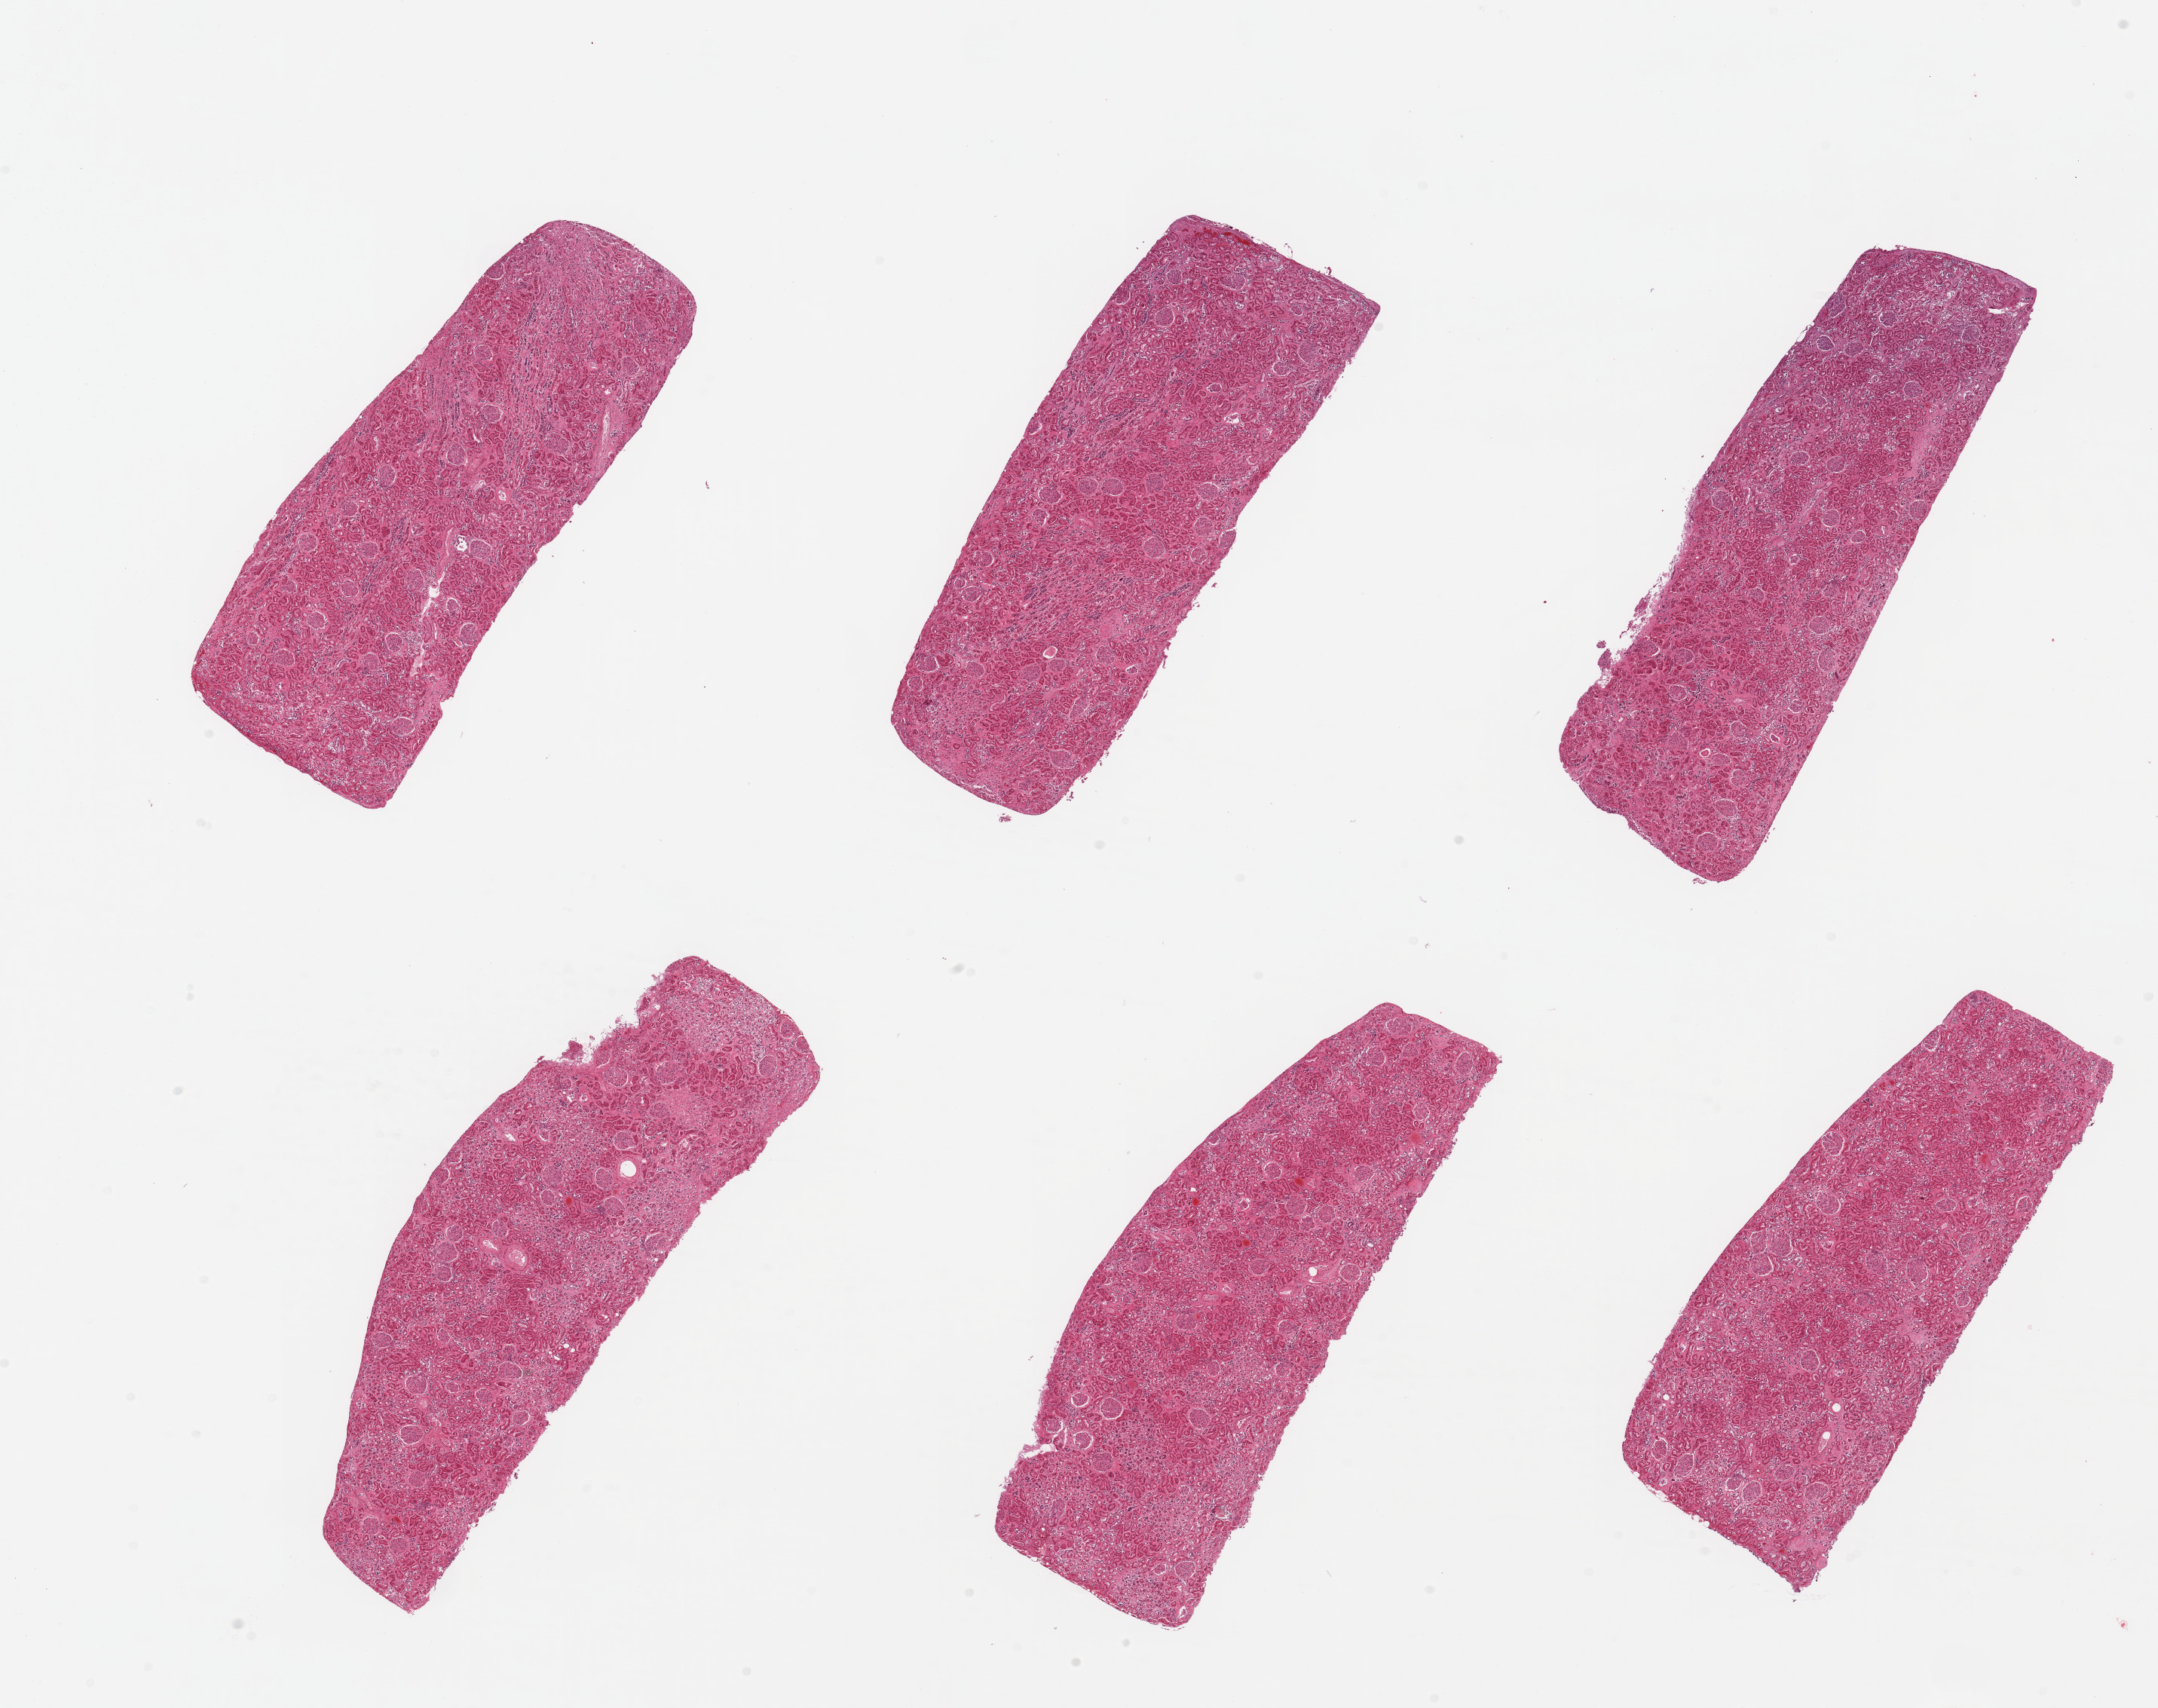
Haematoxylin and eosin whole-slide image, low-resolution overview of the scanned area, about 22.6 x 17.9 mm (acquisition: 20x scan). PAXgene-fixed paraffin-embedded (PFPE) section. Target tissue: renal cortex. Donor tissue sample. Donor: male.
Reviewer comment on this tissue sample: 6 pieces, glomeruli present; advanced tubular autolysis.